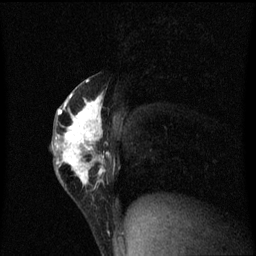
Breast MRI (dynamic contrast-enhanced), one sagittal slice. Slice 31 of 60 in the series (ordered by position). Dynamic contrast-enhanced series, image 2 of 3 at this slice position (ordered by acquisition). 1.5 T. TE 4.2 ms, TR 8.4 ms. 2 mm slice thickness. 256 × 256 image matrix, field of view 200 × 200 mm. Female patient, age 40 years.
Structures marked on this image (semi-automatic segmentation, software-assisted and operator-edited):
- analysis volume of interest (the breast-tissue region the enhancement analysis was run in; not a lesion): box from (x=52, y=76) to (x=112, y=203) px
- tumour enhancement mask (voxels above the 70 % enhancement threshold inside the analysis volume of interest): (x=53, y=80)–(x=109, y=187)